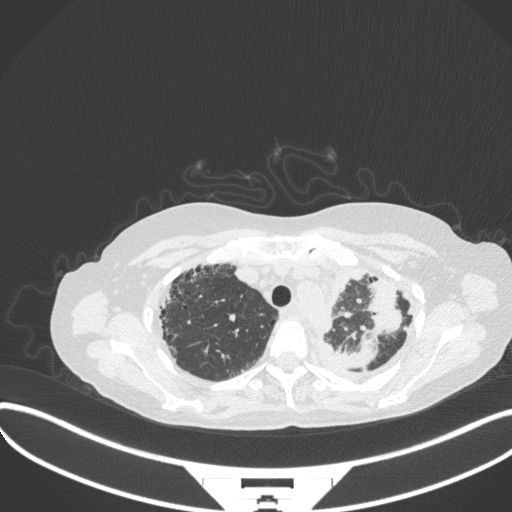
Chest CT, one axial slice. Position 275 of 373 along the scan axis. Reconstruction kernel B31f. 120 kVp. Lung window (W 1500 / L -600 HU). 1 mm slice thickness. 512 × 512 image matrix. Female patient, age 56 years. Case-level facts recorded for this patient, not image findings: clinical TNM (as recorded): T1 N0 M0.
Outlined on this slice (rectangle marked by the reading radiologist):
- lung tumour (recorded histology: adenocarcinoma): bounding box <334,332,378,371> (left, top, right, bottom; pixels)
- lung tumour (recorded histology: adenocarcinoma): <363,281,405,331>